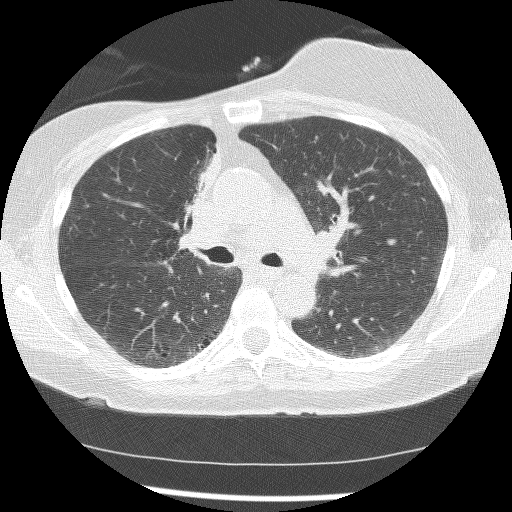
Axial slice from a low-dose chest CT screening exam, baseline annual screen, lung window (W 1500 / L -600 HU), 2.5 mm slice thickness, lung (sharp) reconstruction kernel (BONE), slice 58 of 172 in the series. Female participant, aged 56 years at enrolment. Current smoker at enrolment.
- Lesion marked by an expert reader, box from (x=162, y=152) to (x=217, y=259) px.
- The screening reader recorded 2 non-calcified nodules or masses ≥4 mm on this exam; which of them this box marks is not recorded.
- Official screen result: positive, change unspecified: nodule(s) >= 4 mm or enlarging nodule(s), mass(es), or other non-specific abnormalities suspicious for lung cancer.